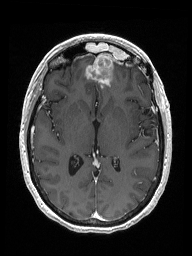
Brain MRI from a brain-tumour surgery series, one axial slice. T1-weighted post-contrast. 1 mm slice thickness. 192 × 256 image matrix, field of view 187 × 250 mm. Case-level facts recorded for this patient, not image findings: histopathology: Metastastic Carcinoma from Breast primary; tumour location: Right Frontal.
Structures marked on this image (expert manual segmentation):
- previous resection cavity: bounding box [x1, y1, x2, y2] px = [87, 56, 114, 80]